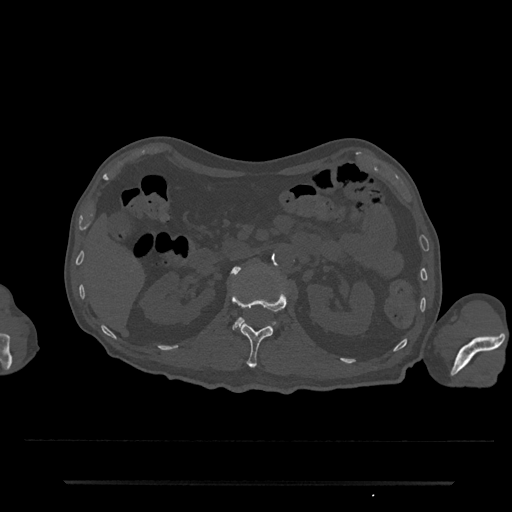
CT including the spine, one axial slice; slice 108 of 797 in the series (ordered by position); reconstruction kernel Br40s/3; bone window (W 1800 / L 400 HU); 512 × 512 image matrix. Male patient, age 74 years. Case-level facts recorded for this patient, not image findings: primary cancer: prostate.
Outlined on this slice (semi-automatic segmentation, software-assisted and operator-edited):
- L1 vertebra: bounding box (x1, y1, x2, y2) in pixels: (231, 289, 288, 368)
- L2 vertebra: (233, 266, 275, 329)